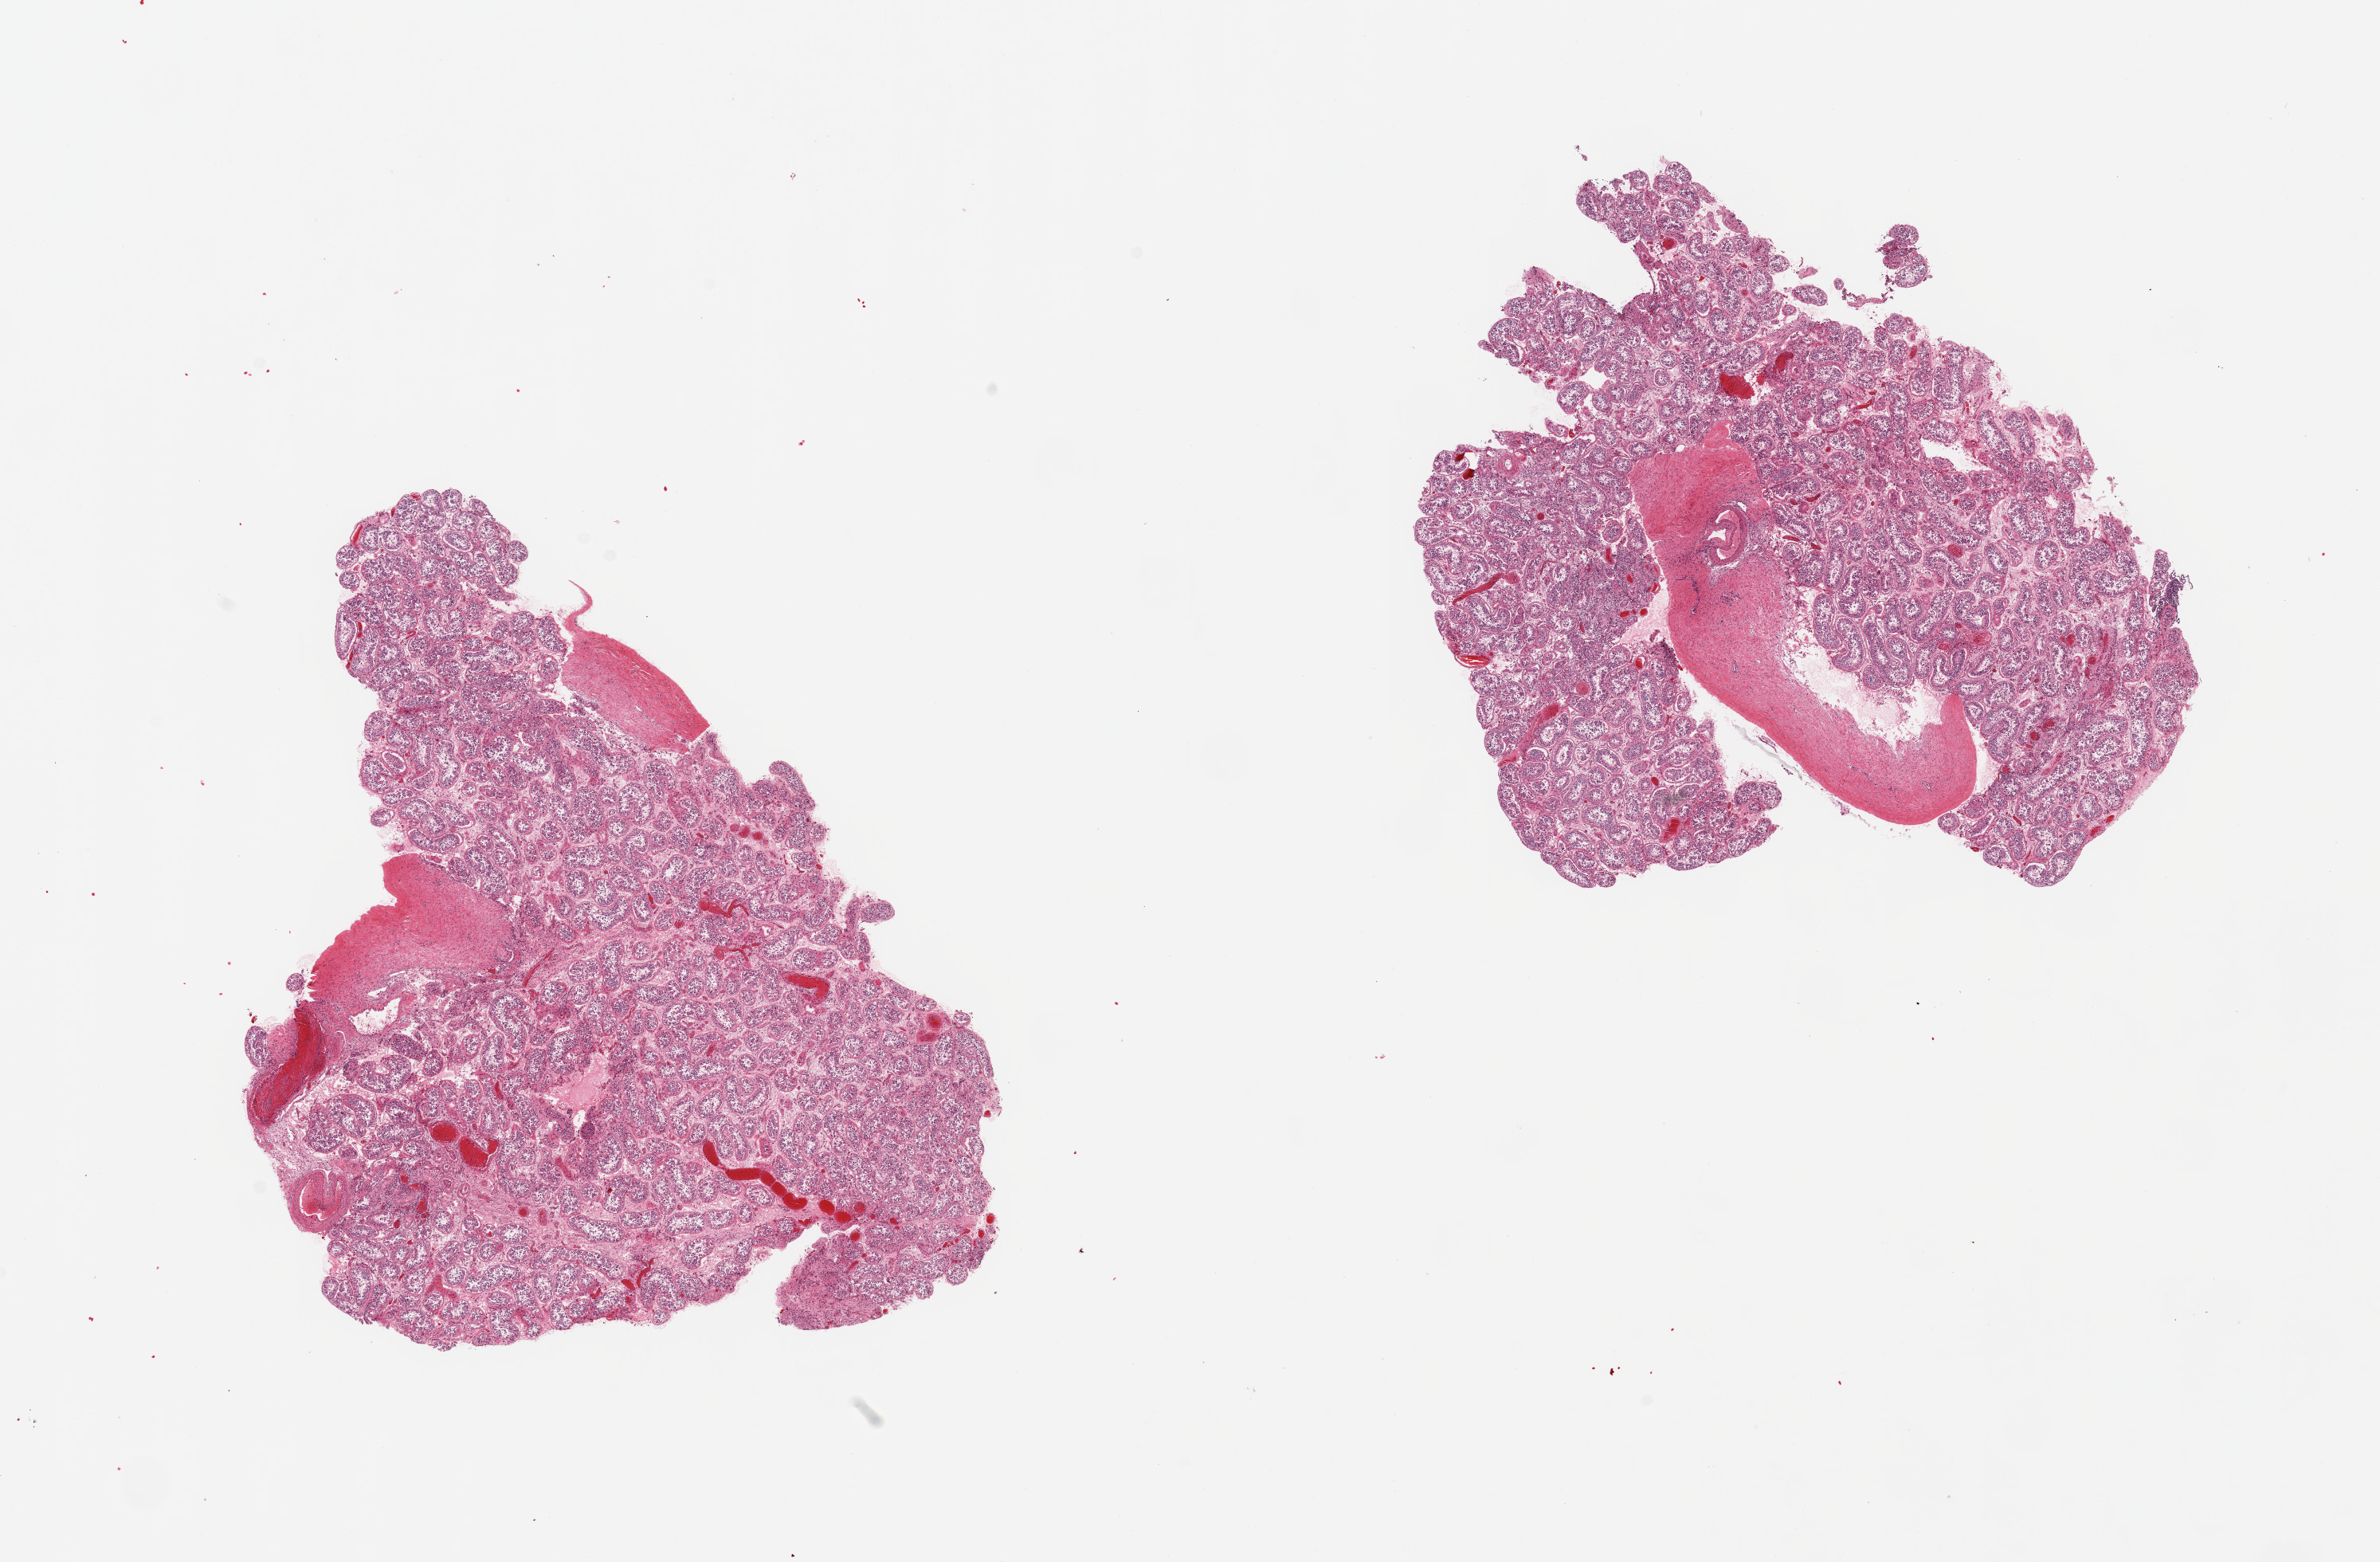
Whole-slide image, H&E stain, brightfield, whole scanned area (about 23.6 x 15.5 mm, acquisition: 20x scan) shown as a low-resolution overview, PAXgene-fixed, paraffin-embedded tissue, target tissue: testis, tissue donor sample. Donor sex: male.
- pathologist's review note for this sample: 2 pieces; spermatogenesis present, congestion